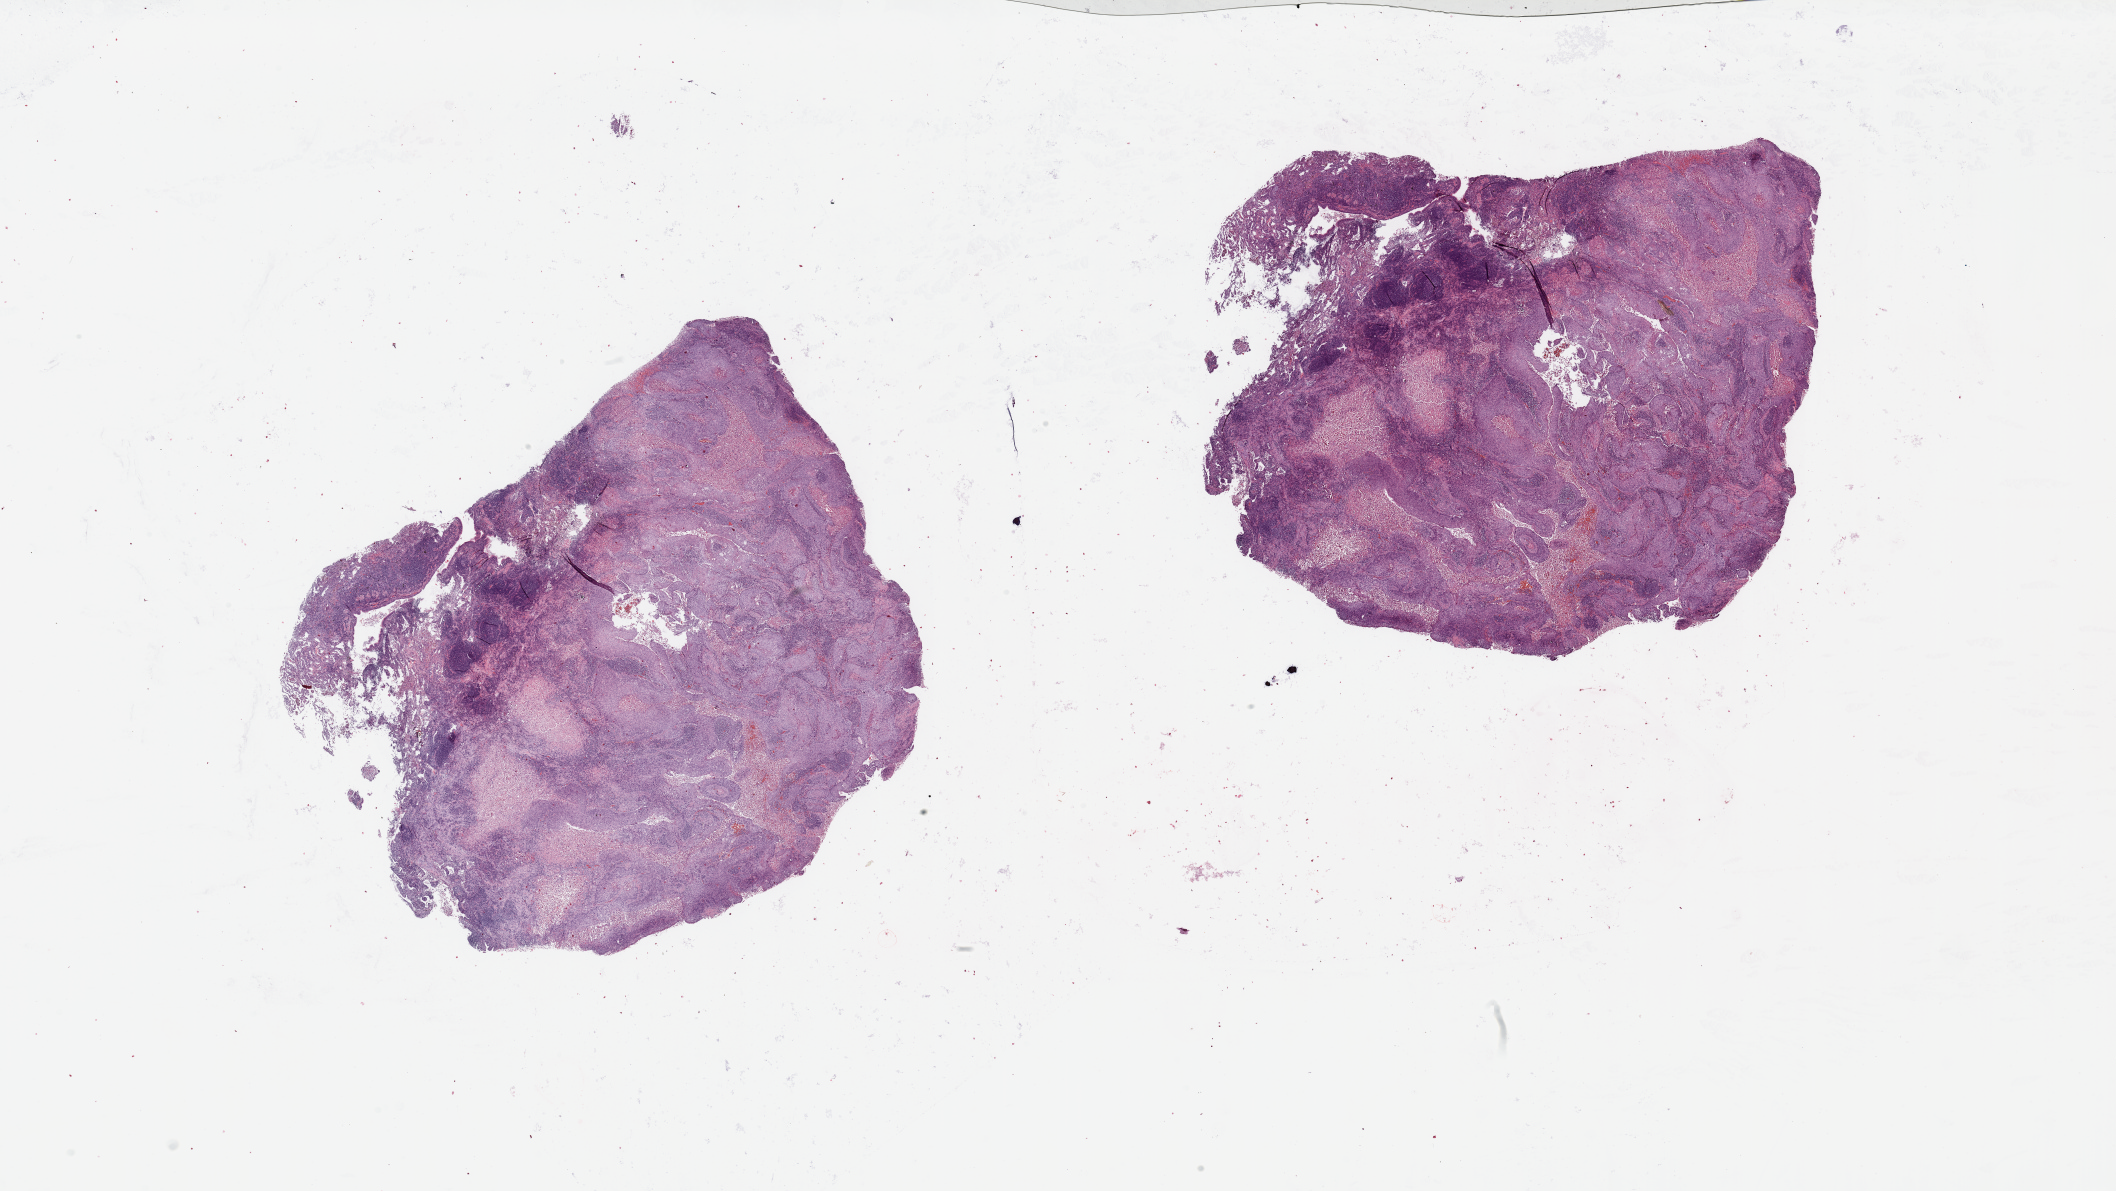
Digitized H&E tissue section (whole slide) — shown as a low-resolution overview of the whole scanned area (about 33.5 x 18.8 mm, from a 20x scan); tumour tissue sample, sampled site: lung. Female, 48 y/o. Histologic grade: G2 (moderately differentiated). Pathologist review of this section (percent, as recorded): tumour nuclei 70%, necrosis 30%.
• primary tumour site (as recorded): left upper lobe
• AJCC pathologic stage: IB
• histologic diagnosis: Squamous cell carcinoma, NOS